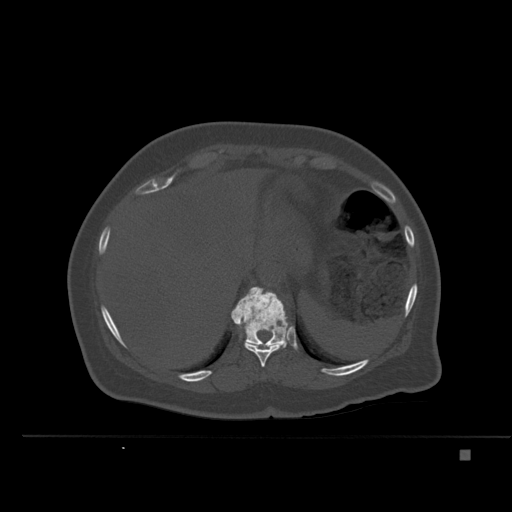
CT including the spine, one axial slice. Position 276 of 477 along the scan axis. Bone window (W 1800 / L 400 HU). 512 × 512 image matrix, field of view 422 × 422 mm. Patient: female, 74 years. From the clinical record (not read from this slice): primary cancer: colon.
Annotated regions visible in this slice (semi-automatically segmented with operator editing):
- T10 vertebra: bounding box [x1, y1, x2, y2] px = [244, 341, 281, 367]
- T11 vertebra: [231, 286, 288, 347]